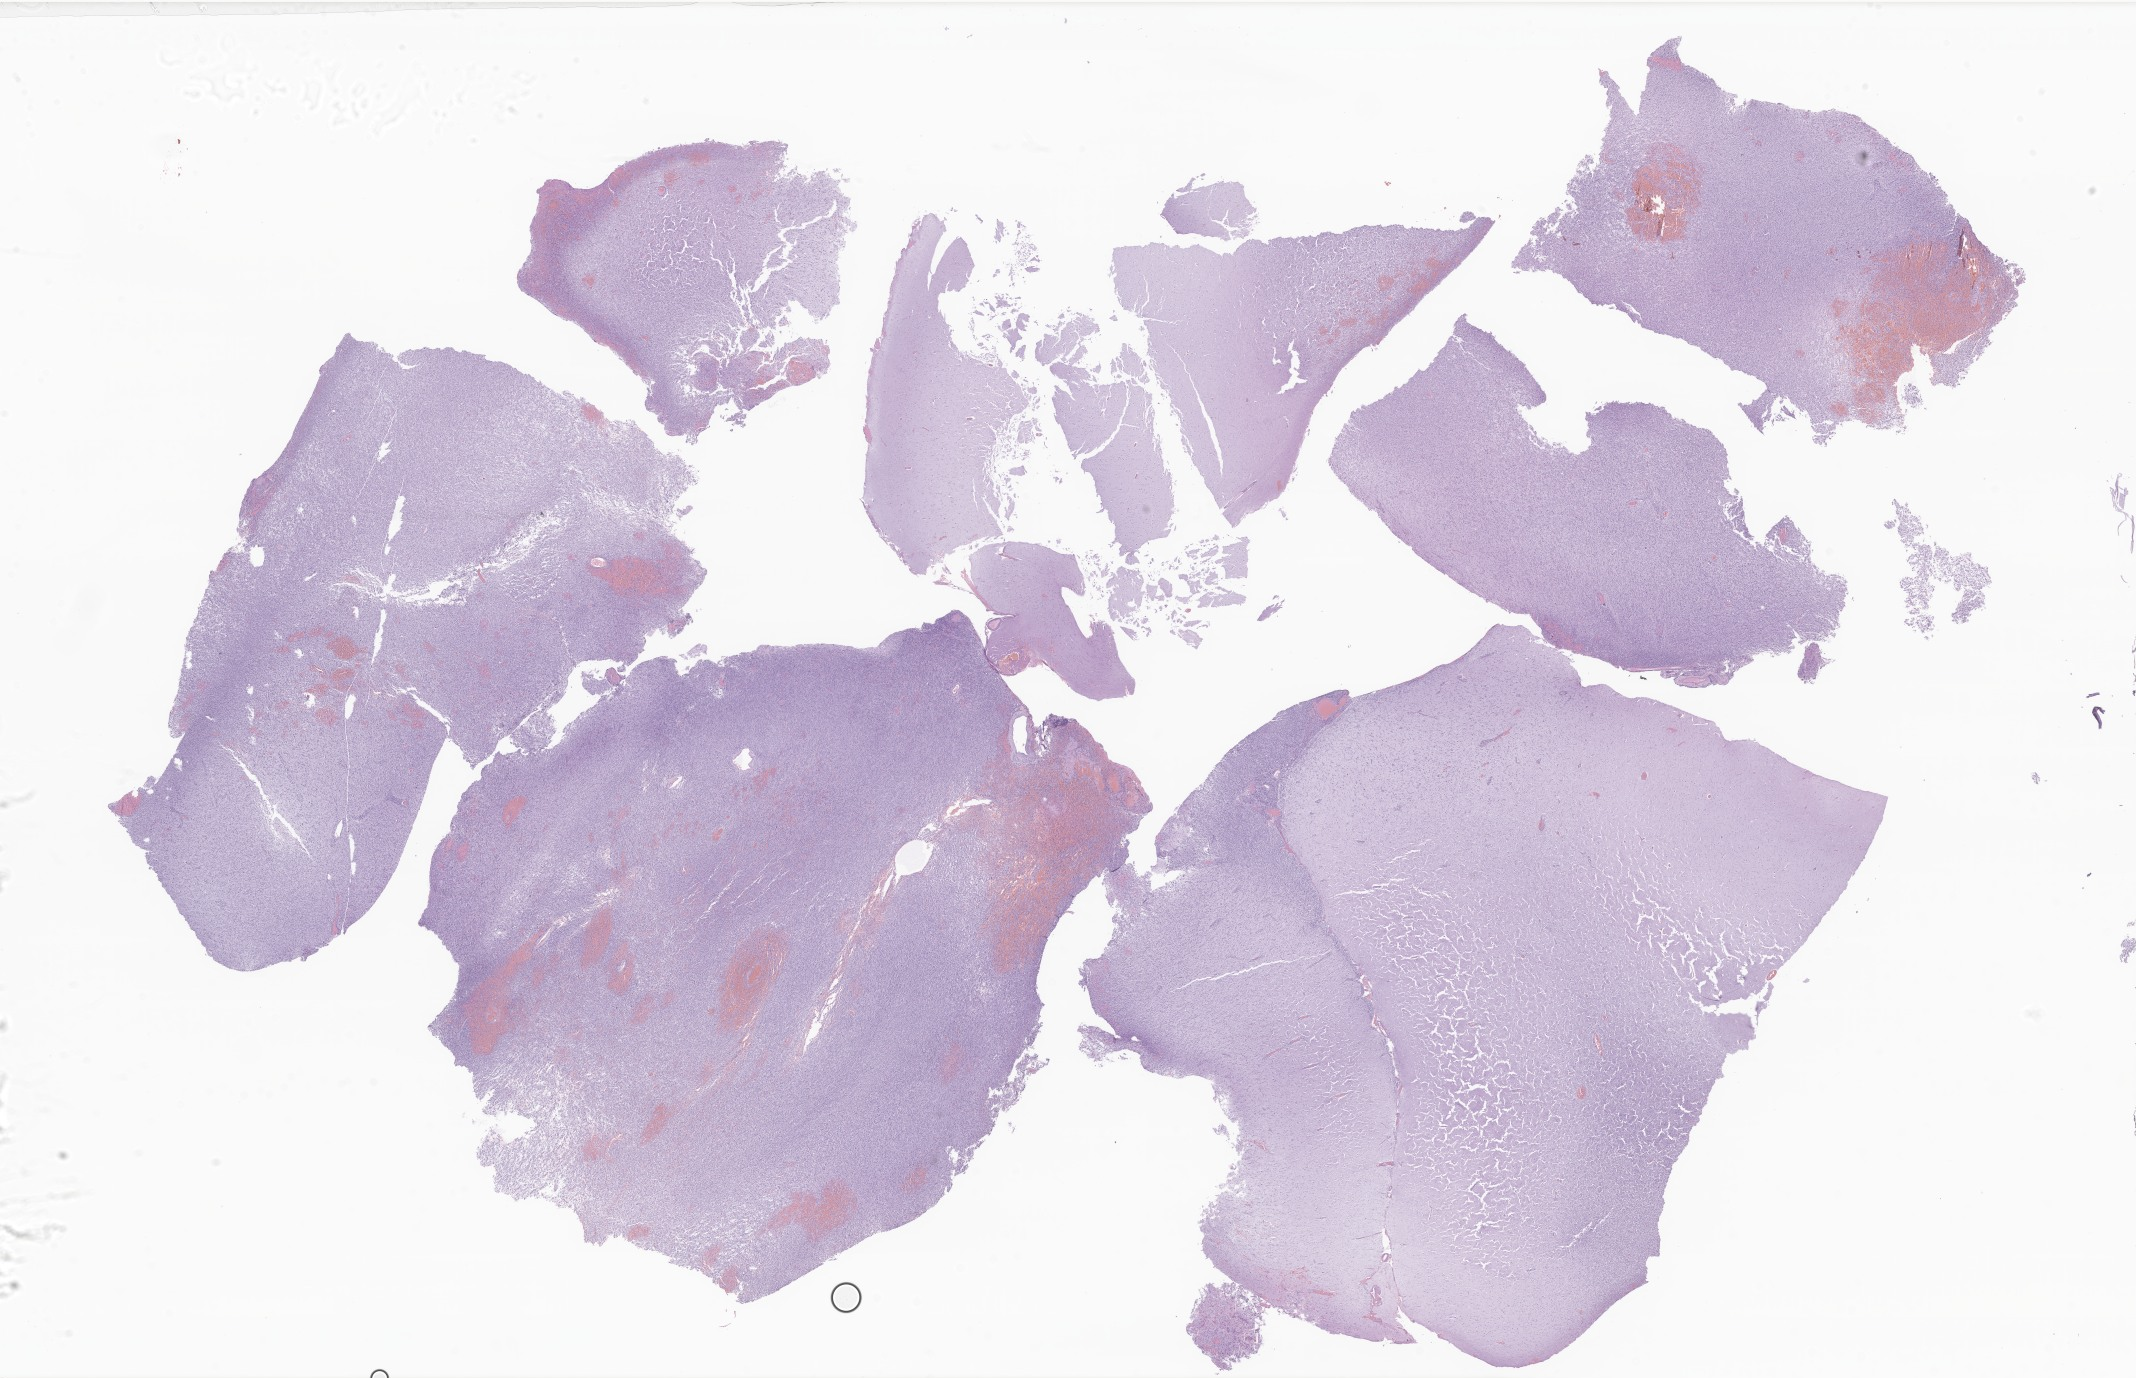
Digitized hematoxylin and eosin (H&E)-stained section of tumor tissue from the brain — whole scanned area (about 36.0 x 23.2 mm) shown as a low-resolution overview; FFPE section. Female patient, age 201 months (16 years 9 months).
Diagnosis (ICD-O-3 morphology term): Glioma, malignant.